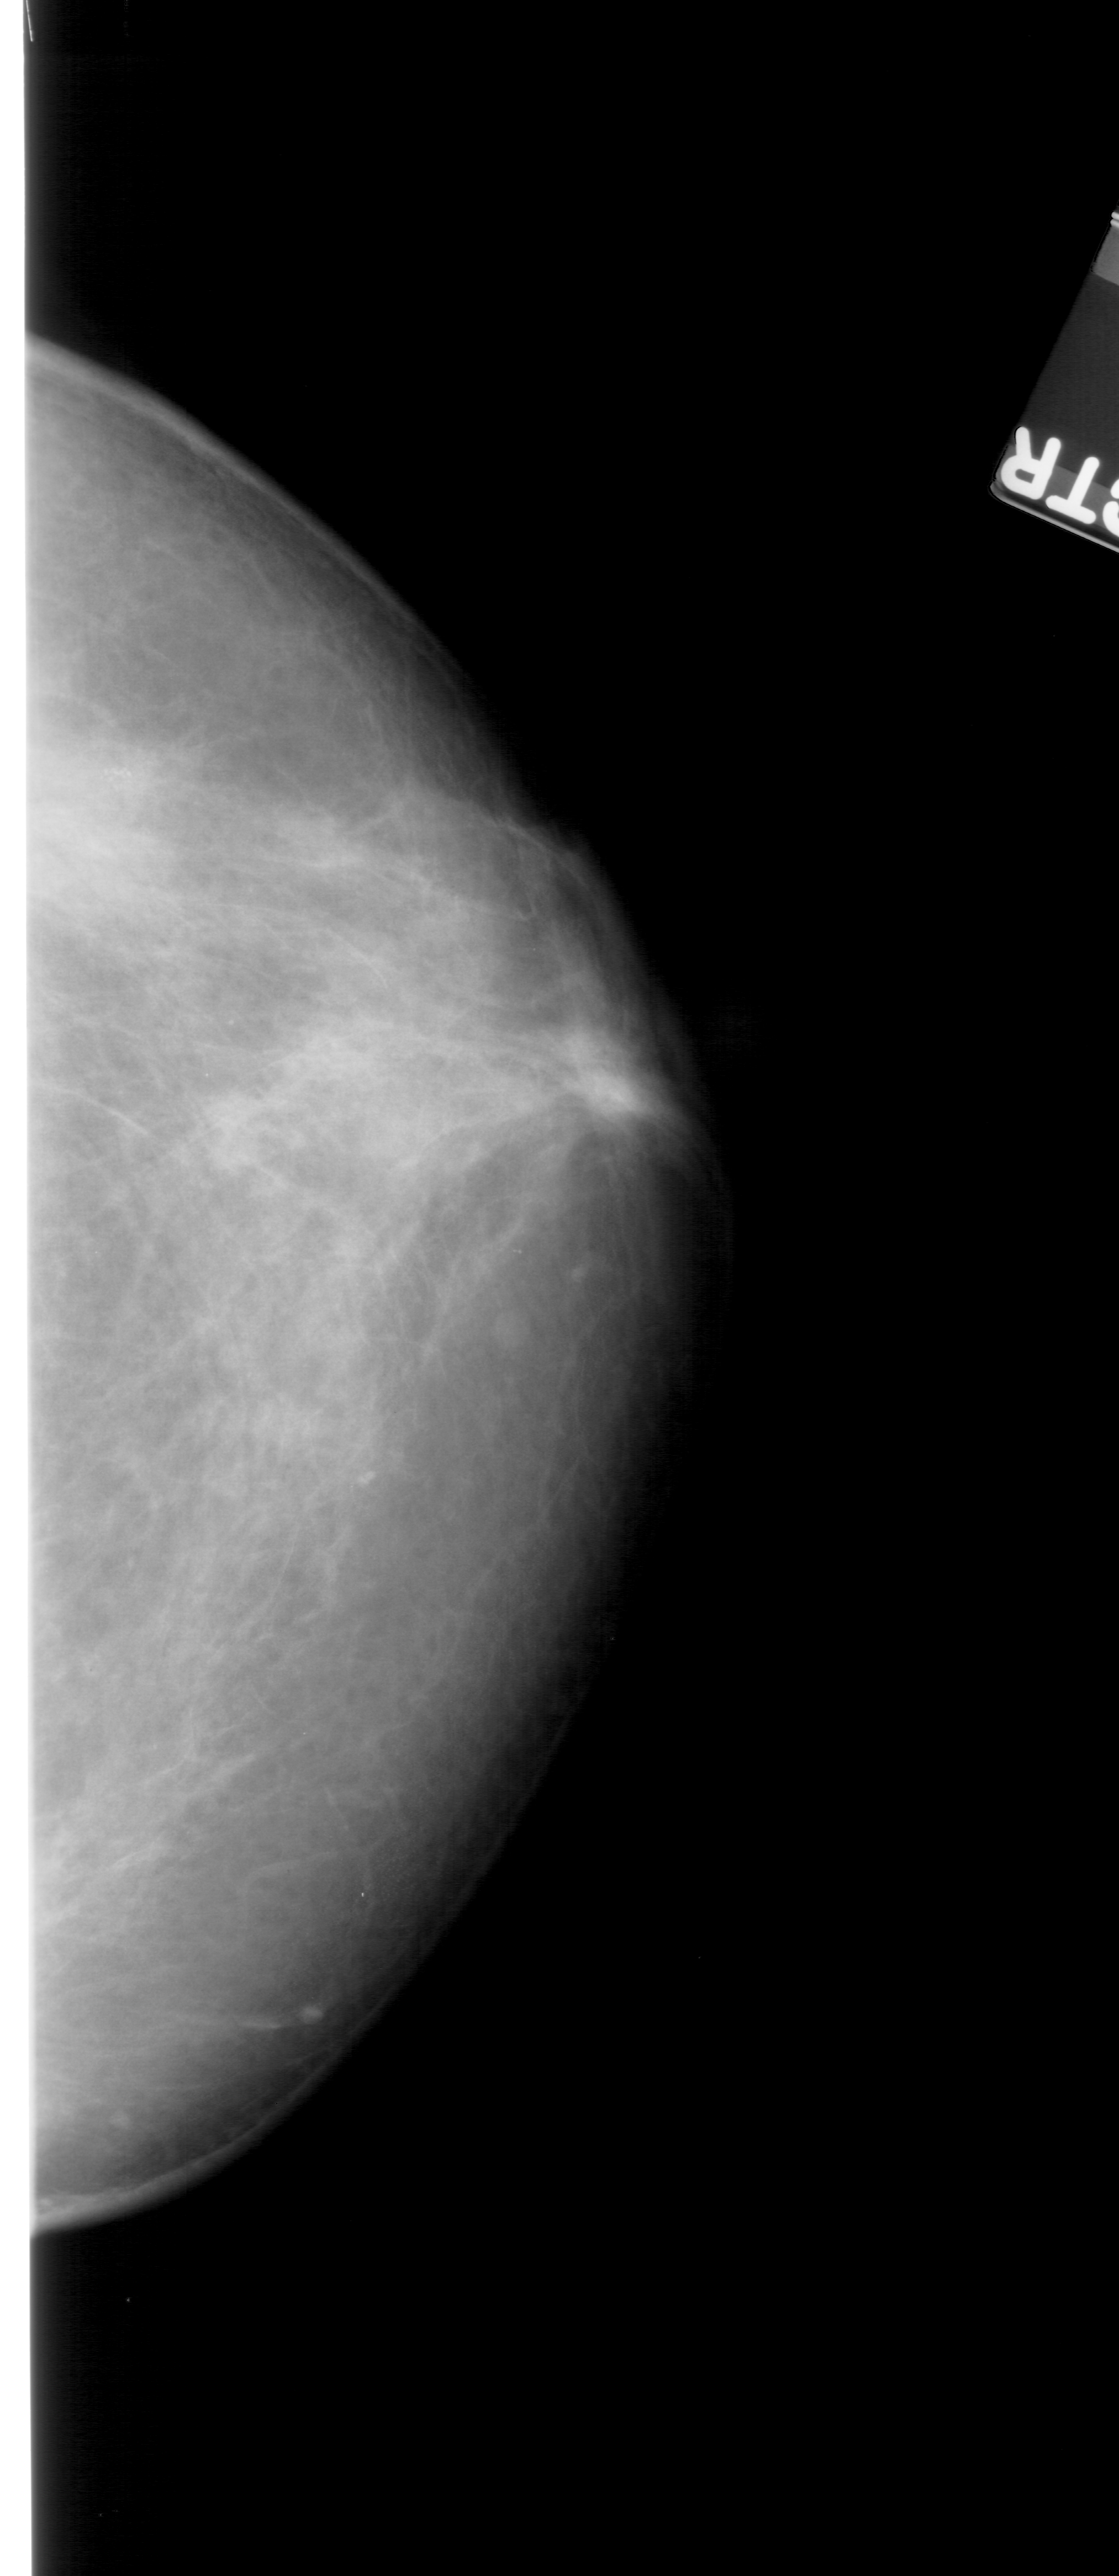
Scanned film-screen mammogram, right breast, CC view, breast composition: extremely dense (BI-RADS density category 4 of 4).
Marked abnormality: calcifications, morphology pleomorphic, distribution clustered; BI-RADS assessment category 4; subtlety rating 4 on a 1 (subtle) to 5 (obvious) scale; pathology result (as recorded, not read from the image): benign.